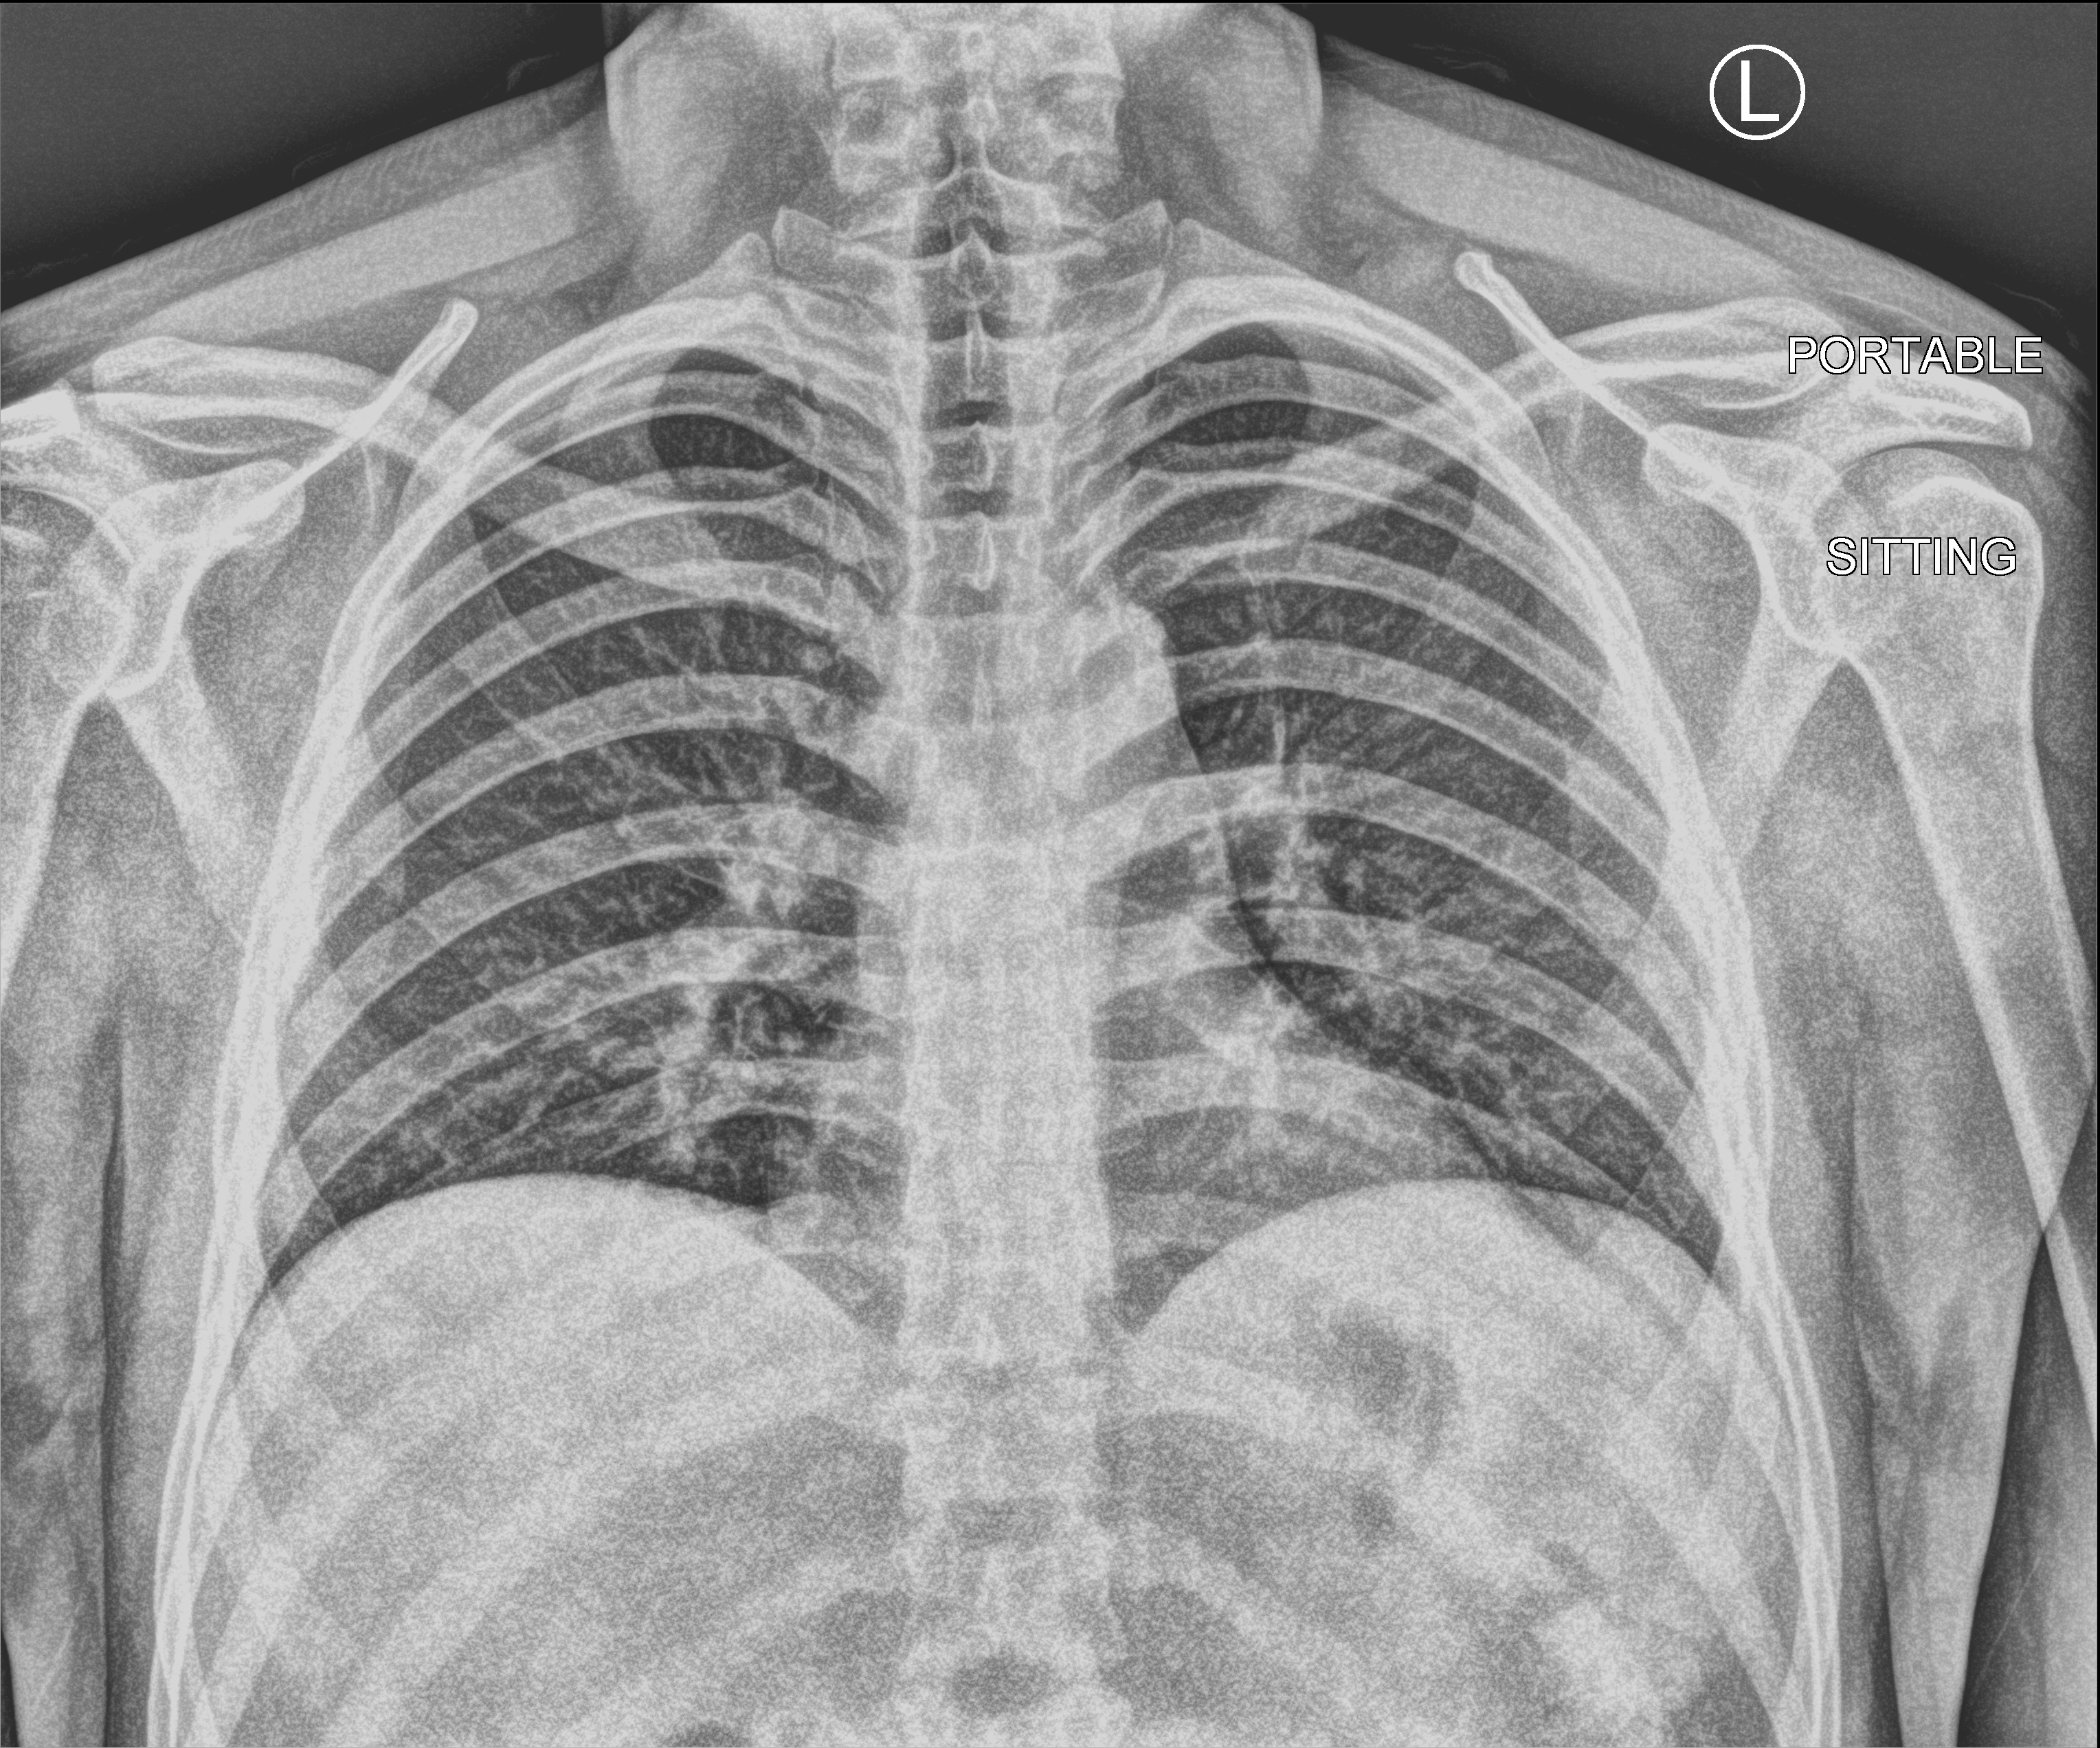
Bedside chest radiograph (computed radiography), anteroposterior (AP) projection. Patient hospitalised with COVID-19; male, aged 18–59 years.
Hospital-stay facts (about this admission, not read from this image; timing relative to this image not recorded): mechanically ventilated during this hospital stay: no.